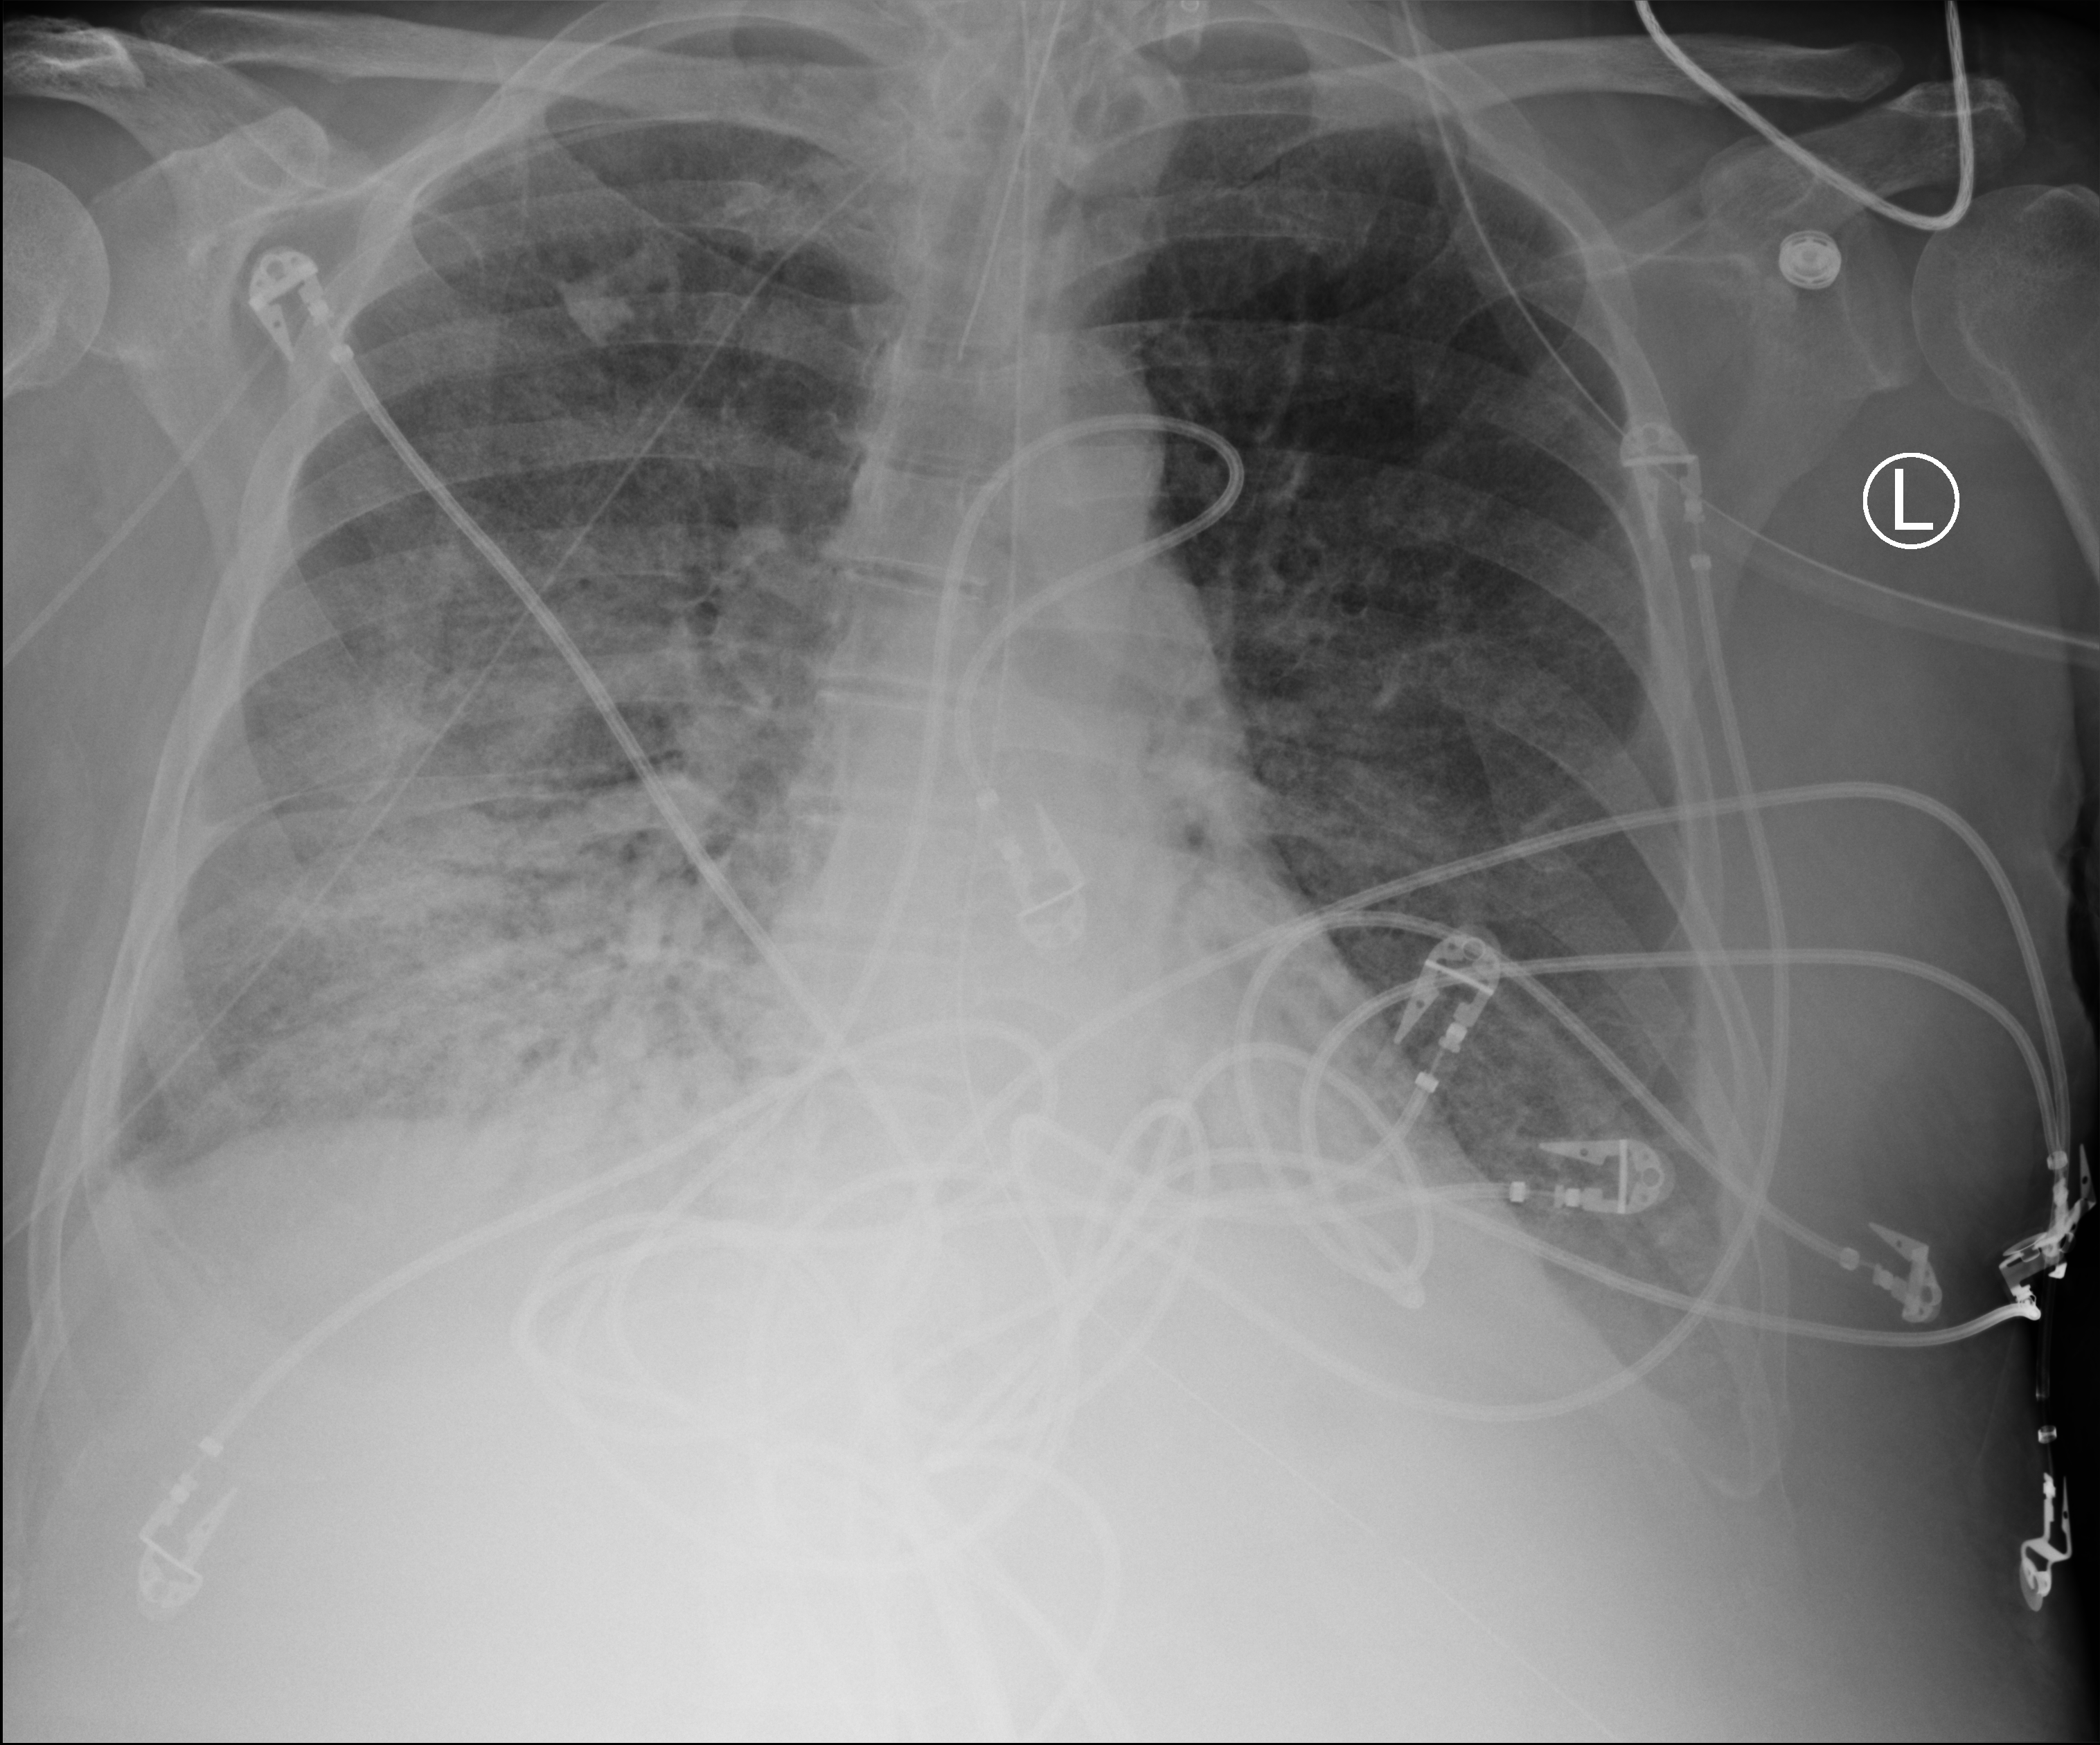
Bedside chest radiograph (computed radiography); anteroposterior (AP) projection. Patient hospitalised with COVID-19; male, aged 60–74 years.
From the hospital-stay record, not from the radiograph (when in the stay this image was taken is not recorded):
- length of hospital stay: 24 days
- mechanically ventilated during this hospital stay: yes
- hypertension (admission record): no